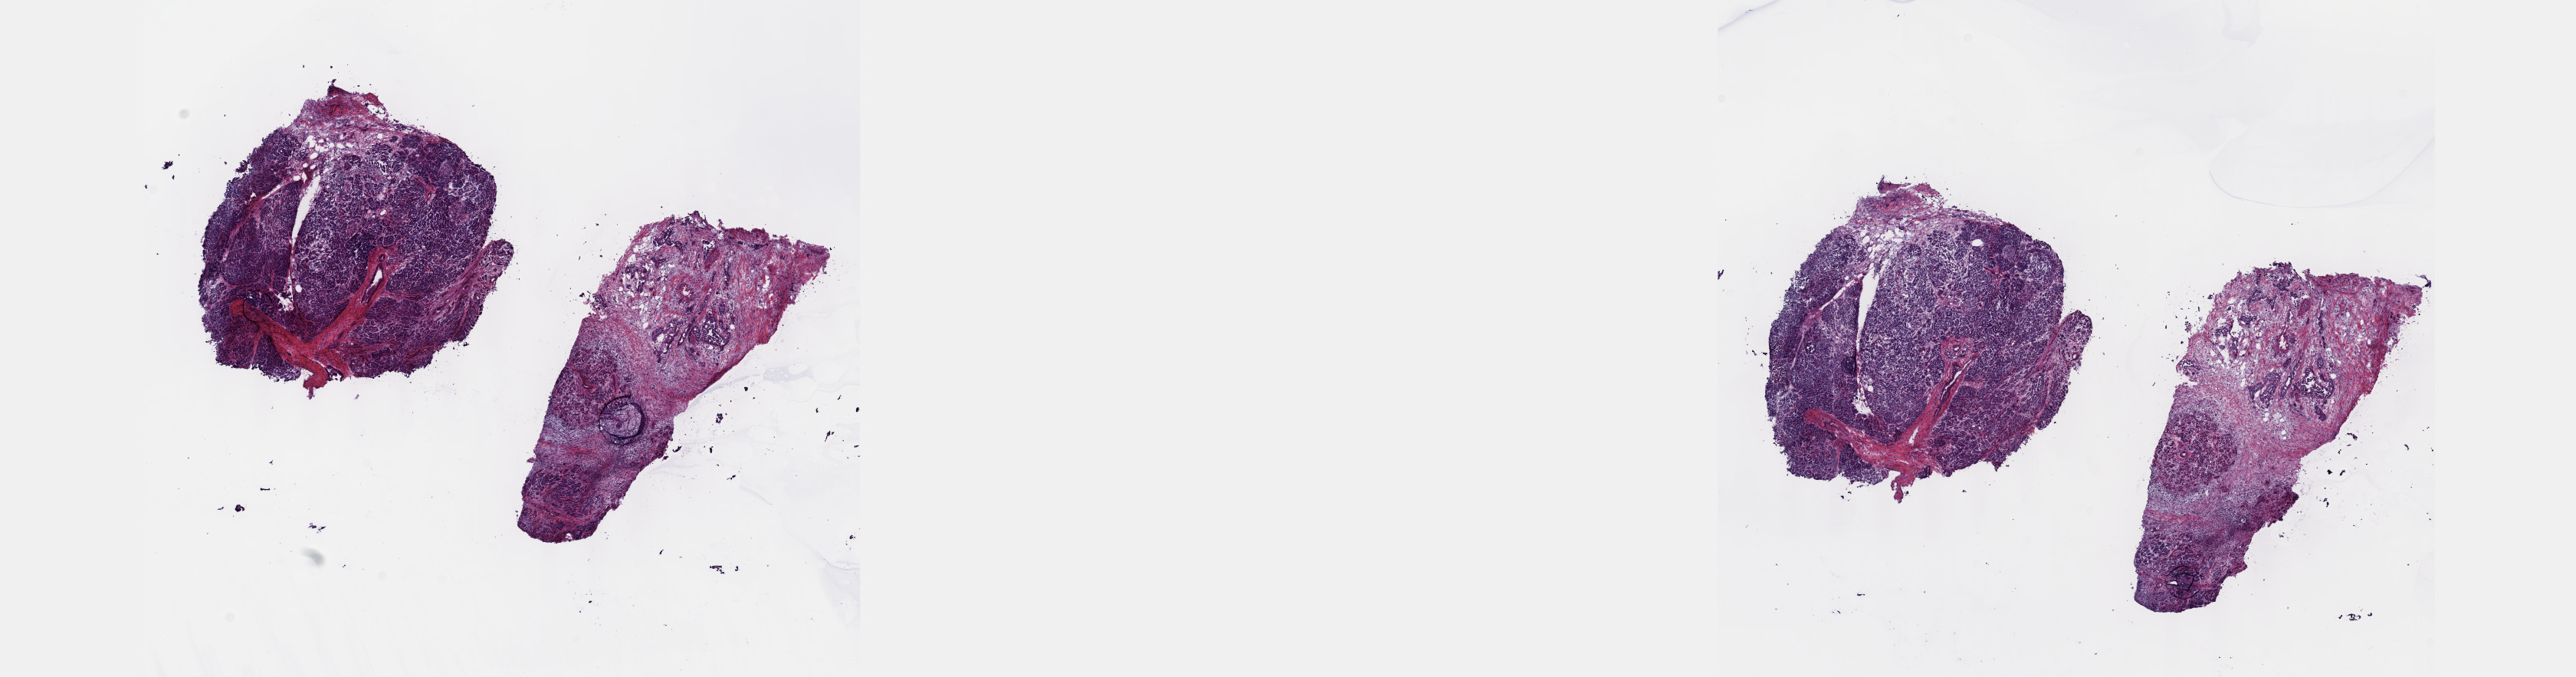
Whole-slide histology image, Hematoxylin and eosin (H&E) stained, shown as a low-resolution overview of the whole scanned area (about 27.2 x 7.1 mm, slide scanned at 40x); frozen section from the top of the tissue portion; sample: primary tumour, pancreas. Male patient; age at initial diagnosis 67 years. Histologic grade: G2 (moderately differentiated). Composition of this section per pathologist review: tumour cells 20%, tumour nuclei 10%, normal cells 80%, stromal cells 0%, necrosis 0%. Inflammatory infiltration, as recorded: lymphocyte infiltration 5%, monocyte infiltration 0%, neutrophil infiltration 0%.
TNM: T2 N0 M0. Lymph nodes positive (case pathology): 0 of 15 examined. Diagnosis: Infiltrating duct carcinoma, NOS. AJCC pathologic stage: IB (7th edition).